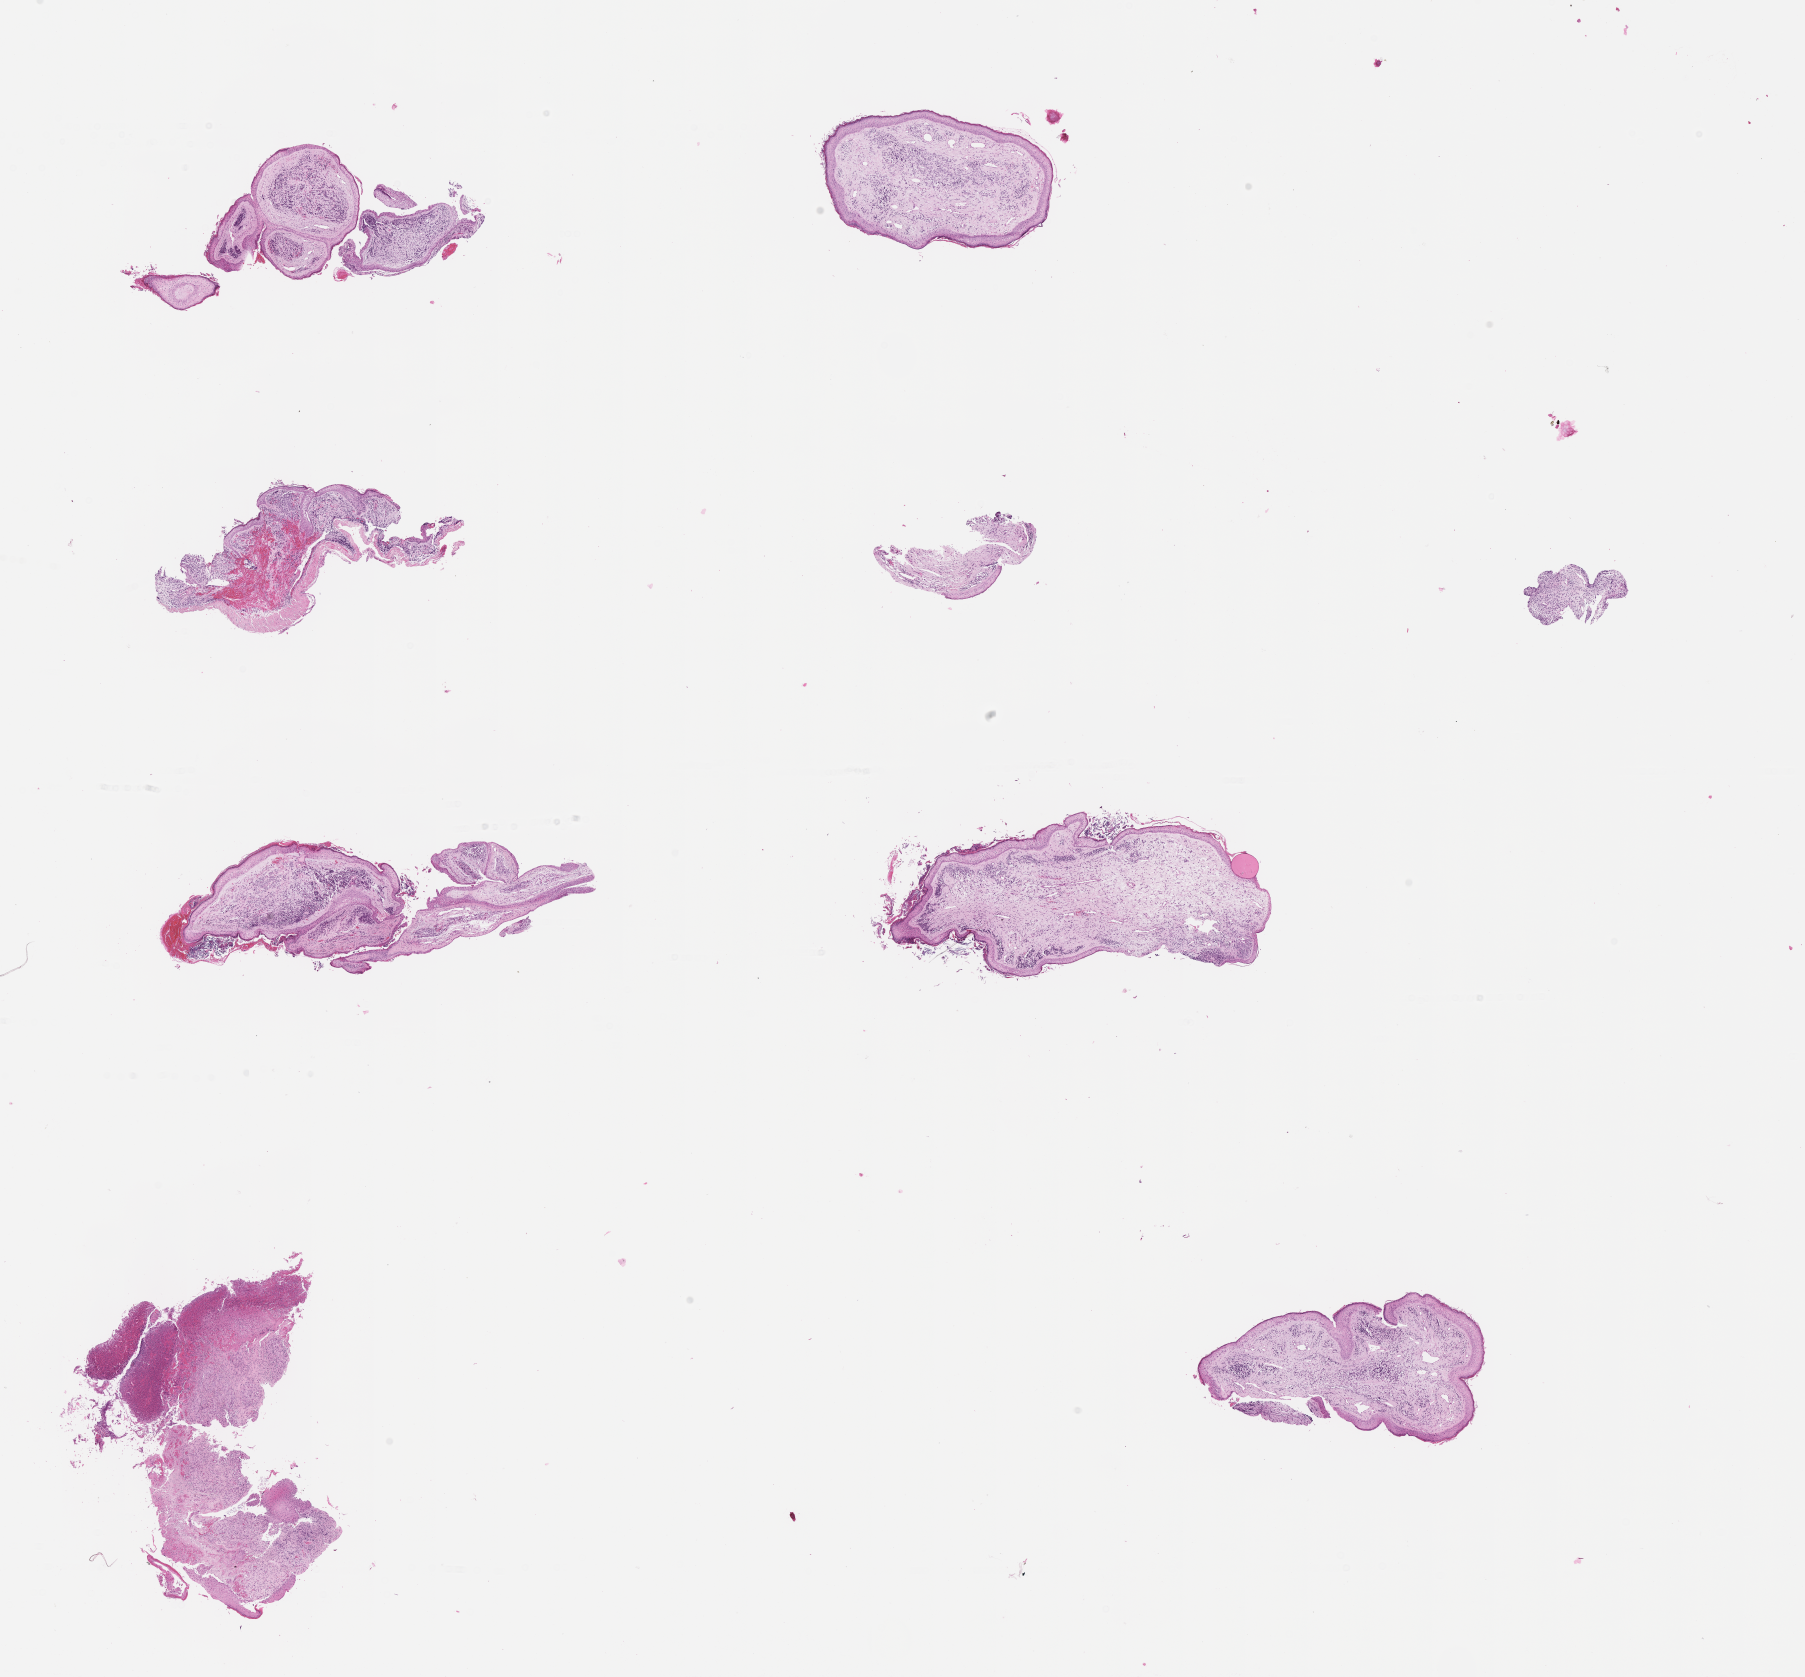
Whole-slide image, H&E stain of tumor tissue, a low-resolution overview of the entire scanned area, about 14.6 x 13.6 mm. FFPE section. Site: soft tissue, ear-left (ear canal). Patient: female, age 5.5 years at diagnosis.
Metastatic status at presentation (as recorded): metastatic (confirmed). Diagnosis: rhabdomyosarcoma; histological classification: embryonal rhabdomyosarcoma. Primary site (case record): middle ear (PM). Stage (as recorded): 4.